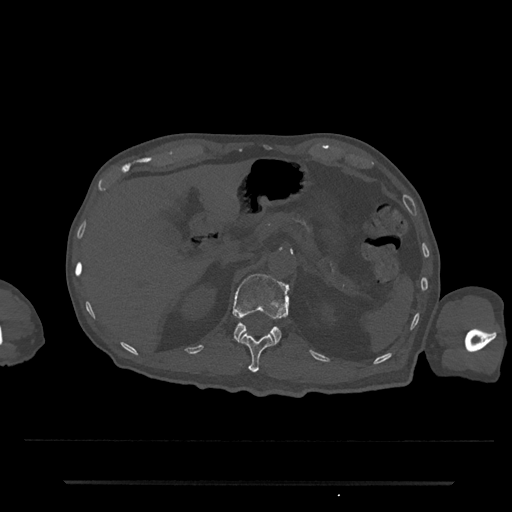
CT including the spine, one axial slice. Slice 165 of 797 in the series (ordered by position). Reconstruction kernel Br40s/3. Bone window (W 1800 / L 400 HU). 0.5 mm slice thickness. 512 × 512 image matrix. Patient: male, 74 years. From the clinical record (not read from this slice): primary cancer: prostate.
Structures marked on this image (semi-automatic segmentation, software-assisted and operator-edited):
- L1 vertebra: bounding box (x1, y1, x2, y2) in pixels: (233, 274, 290, 345)
- T12 vertebra: (240, 333, 273, 373)